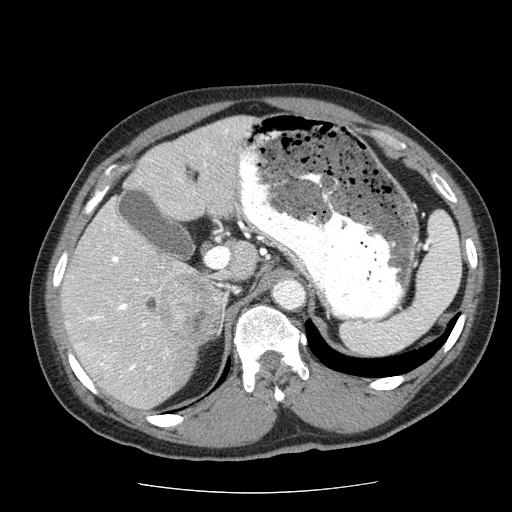
Contrast-enhanced abdominal CT (liver protocol), one axial slice. Slice 34 of 85 in the series (ordered by position). Reconstruction kernel STANDARD. Soft-tissue window (W 400 / L 40 HU). 2.5 mm slice thickness. 512 × 512 image matrix, field of view 360 × 360 mm. Case-level facts recorded for this patient, not image findings: diagnosis: hepatocellular carcinoma (patient treated with transarterial chemoembolisation; whether this scan precedes or follows treatment is not stated here); TNM stage (as recorded): Stage-IIIA; Child-Pugh class: A; tumour differentiation: well differentiated; tumour nodularity: multinodular.
Structures marked on this image (semi-automatic segmentation, software-assisted and operator-edited):
- abdominal aorta: bounding box [x1, y1, x2, y2] px = [276, 279, 304, 307]
- liver parenchyma outside the tumour (the mass and vessels are separate outlines, so this box may not span the whole liver): [60, 116, 270, 408]
- mass: [144, 272, 223, 343]
- liver vessels: [67, 129, 271, 371]